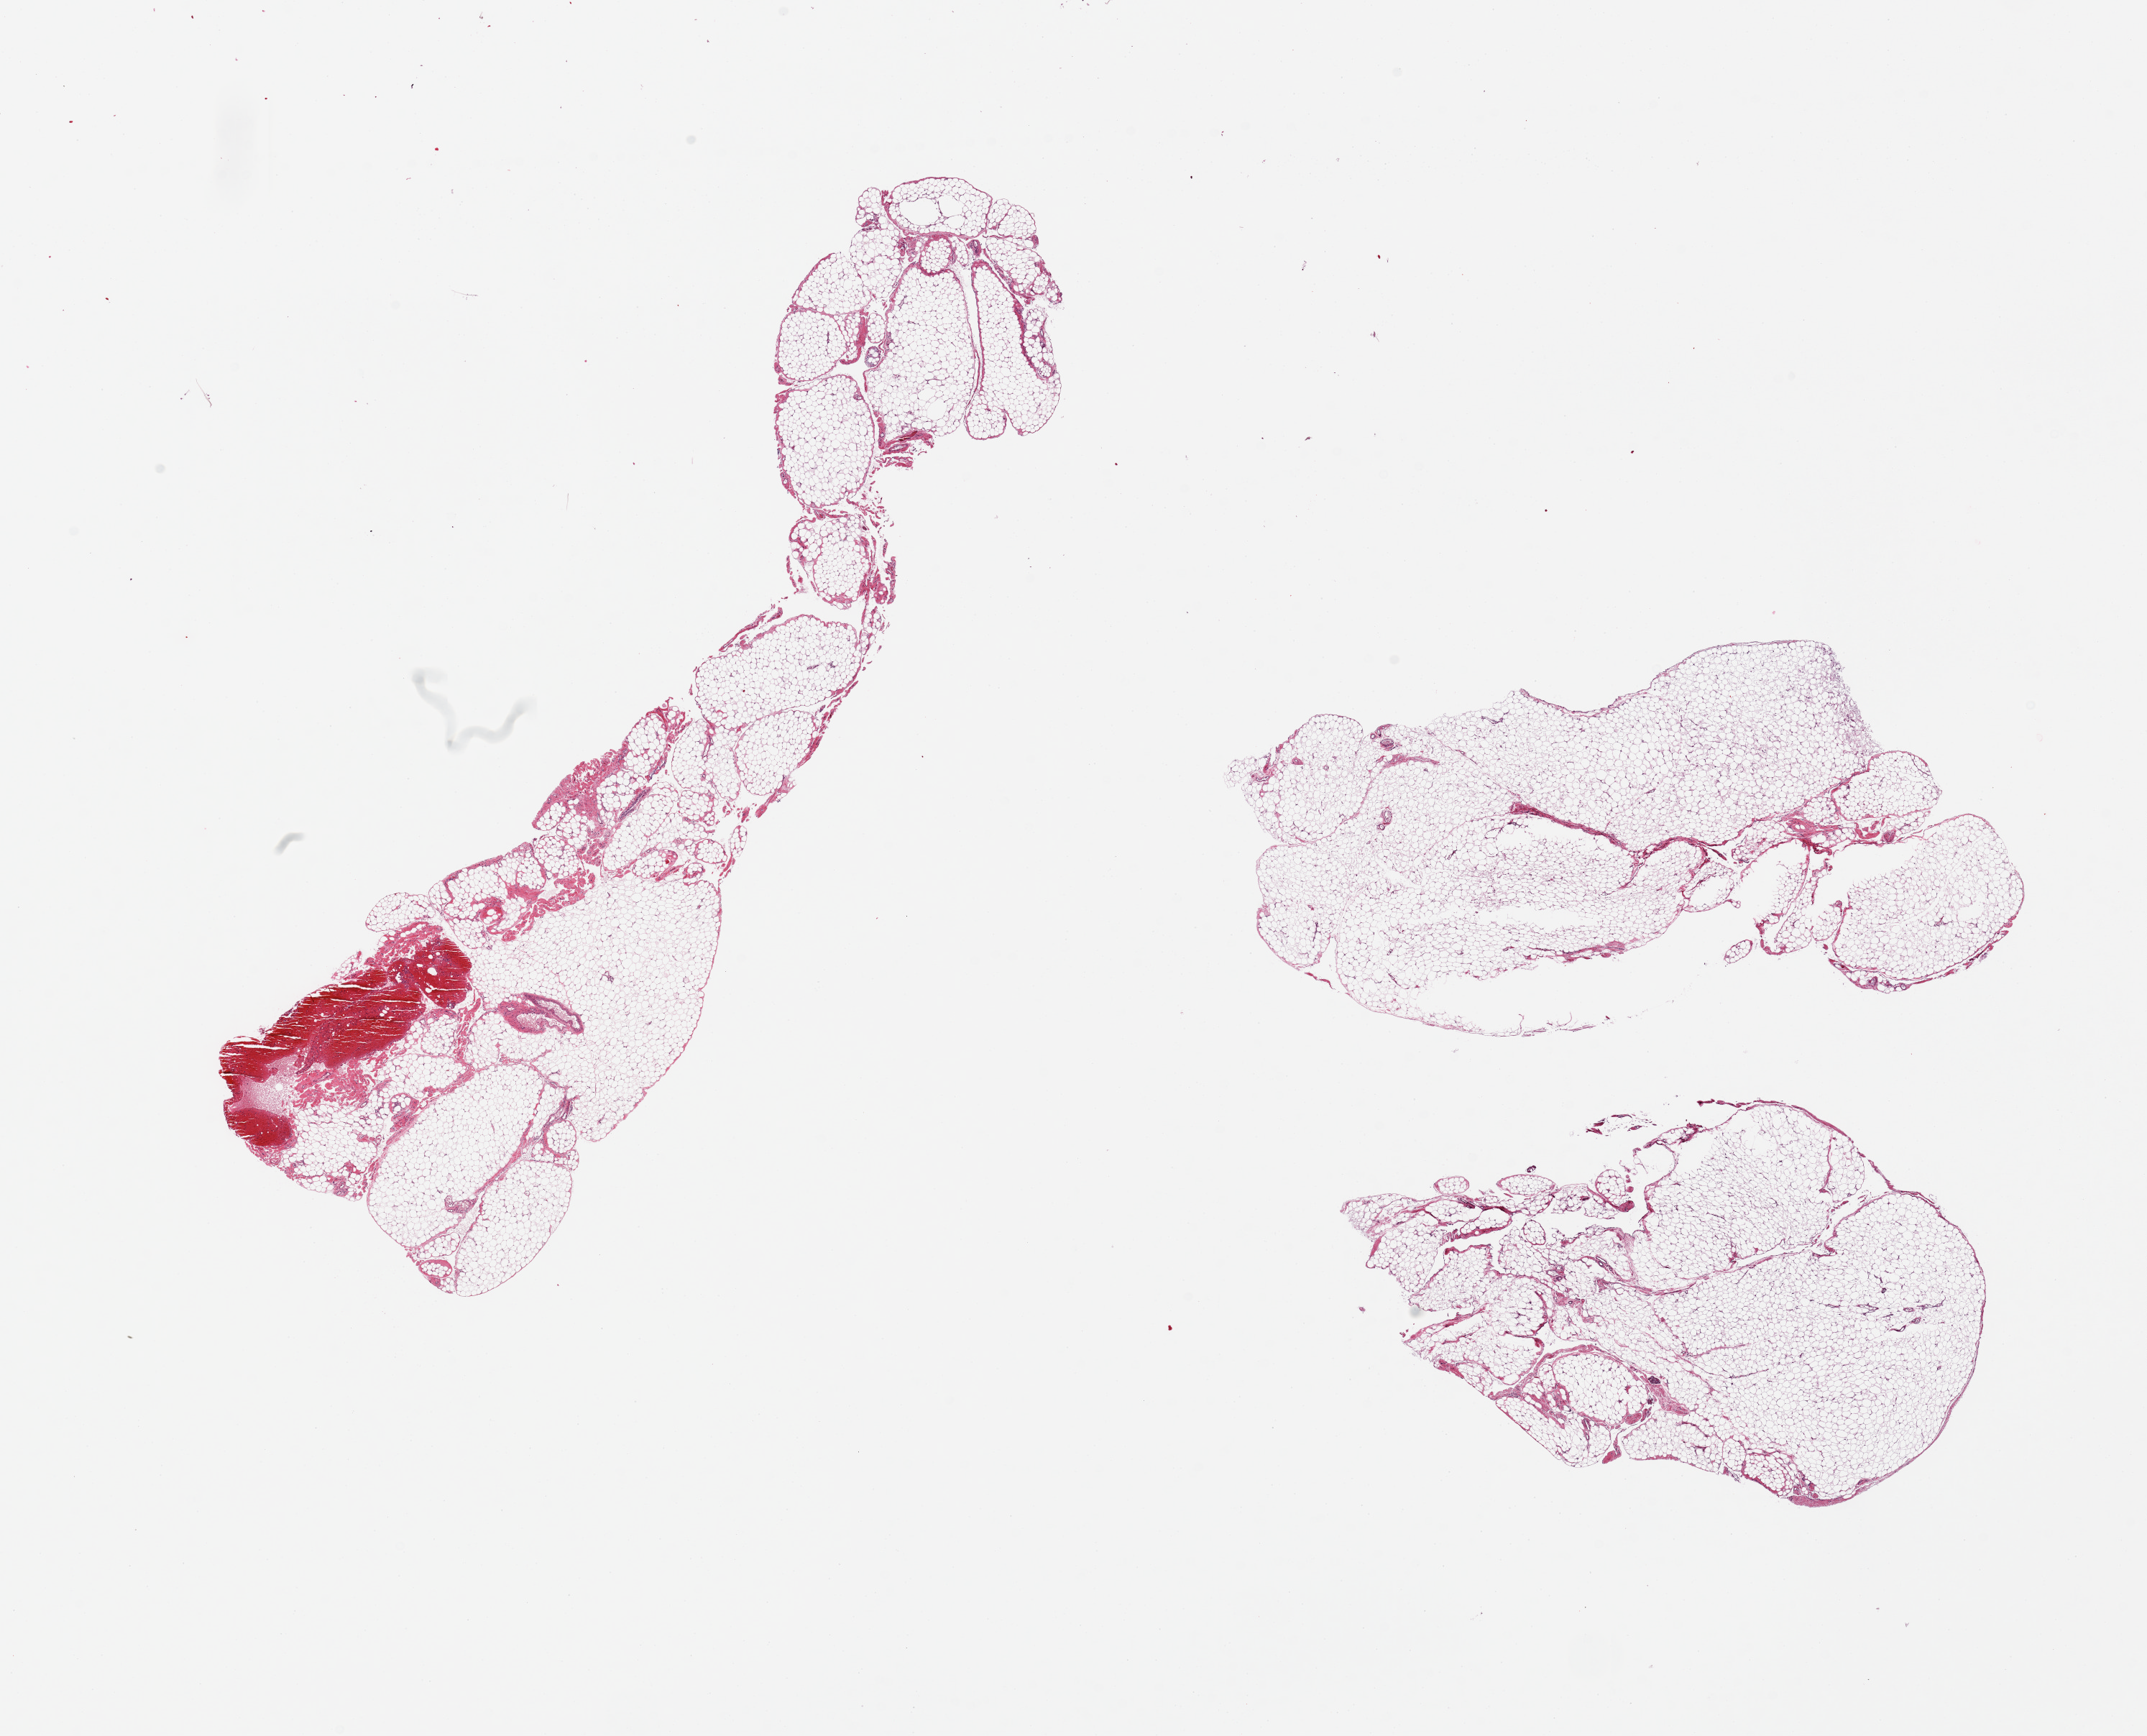
Whole-slide image, haematoxylin and eosin stain, low-resolution overview of the scanned area, about 23.6 x 19.1 mm, PAXgene-fixed, paraffin-embedded tissue, section of omentum (target tissue), donor tissue sample. Male donor.
Review note (as recorded): 3 pieces, fibrosis/vessels are ~5% tissue.